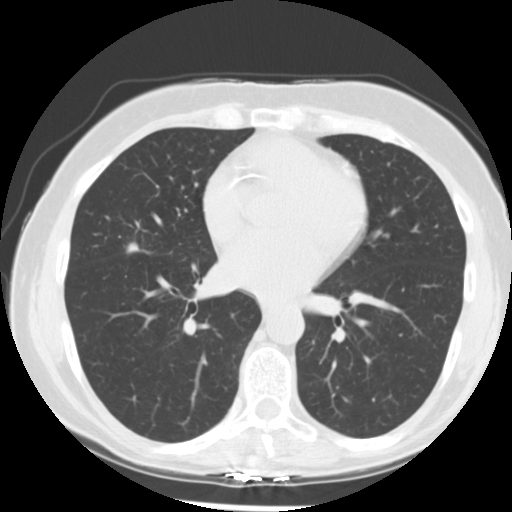
Low-dose screening chest CT, axial slice; first (baseline) screen; lung window (W 1500 / L -600 HU); 2.5 mm slice thickness; slice 129 of 255 in the series. Female participant, aged 66 years at enrolment. Former smoker at enrolment.
Expert-annotated lung lesion, bounding box <115,228,168,266> (left, top, right, bottom; pixels). Screening reader's record for this exam (one nodule recorded; not confirmed to be the boxed lesion): non-calcified nodule or mass ≥4 mm, right middle lobe, 15 × 13 mm, poorly defined margins, soft tissue attenuation. Official screen result: positive, change unspecified: nodule(s) >= 4 mm or enlarging nodule(s), mass(es), or other non-specific abnormalities suspicious for lung cancer. Participant outcome: lung cancer diagnosed 27 days after this screen — adenocarcinoma, NOS, right middle lobe, undifferentiated (G4), stage IIIA (AJCC 6th edition), 18 mm at pathology.